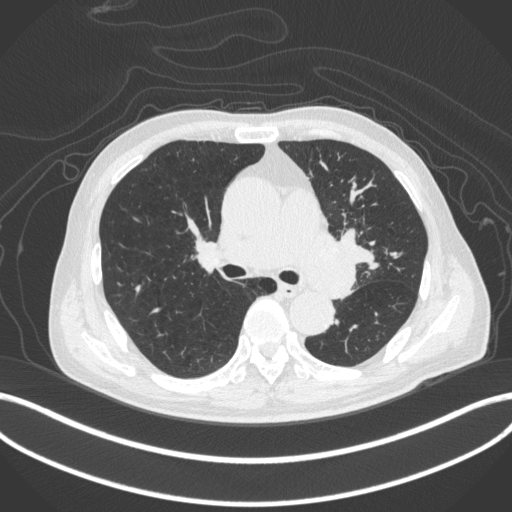
Chest CT, one axial slice. Slice 262 of 420 in the series (ordered by position). 120 kVp. Lung window (W 1500 / L -600 HU). 512 × 512 image matrix, field of view 400 × 400 mm. Male patient, age 77 years. From the clinical record (not read from this slice): clinical TNM (as recorded): T3 N1 M0.
Structures marked on this image (rectangle marked by the reading radiologist):
- lung tumour (recorded histology: adenocarcinoma): bounding box (x1, y1, x2, y2) in pixels: (299, 225, 368, 300)